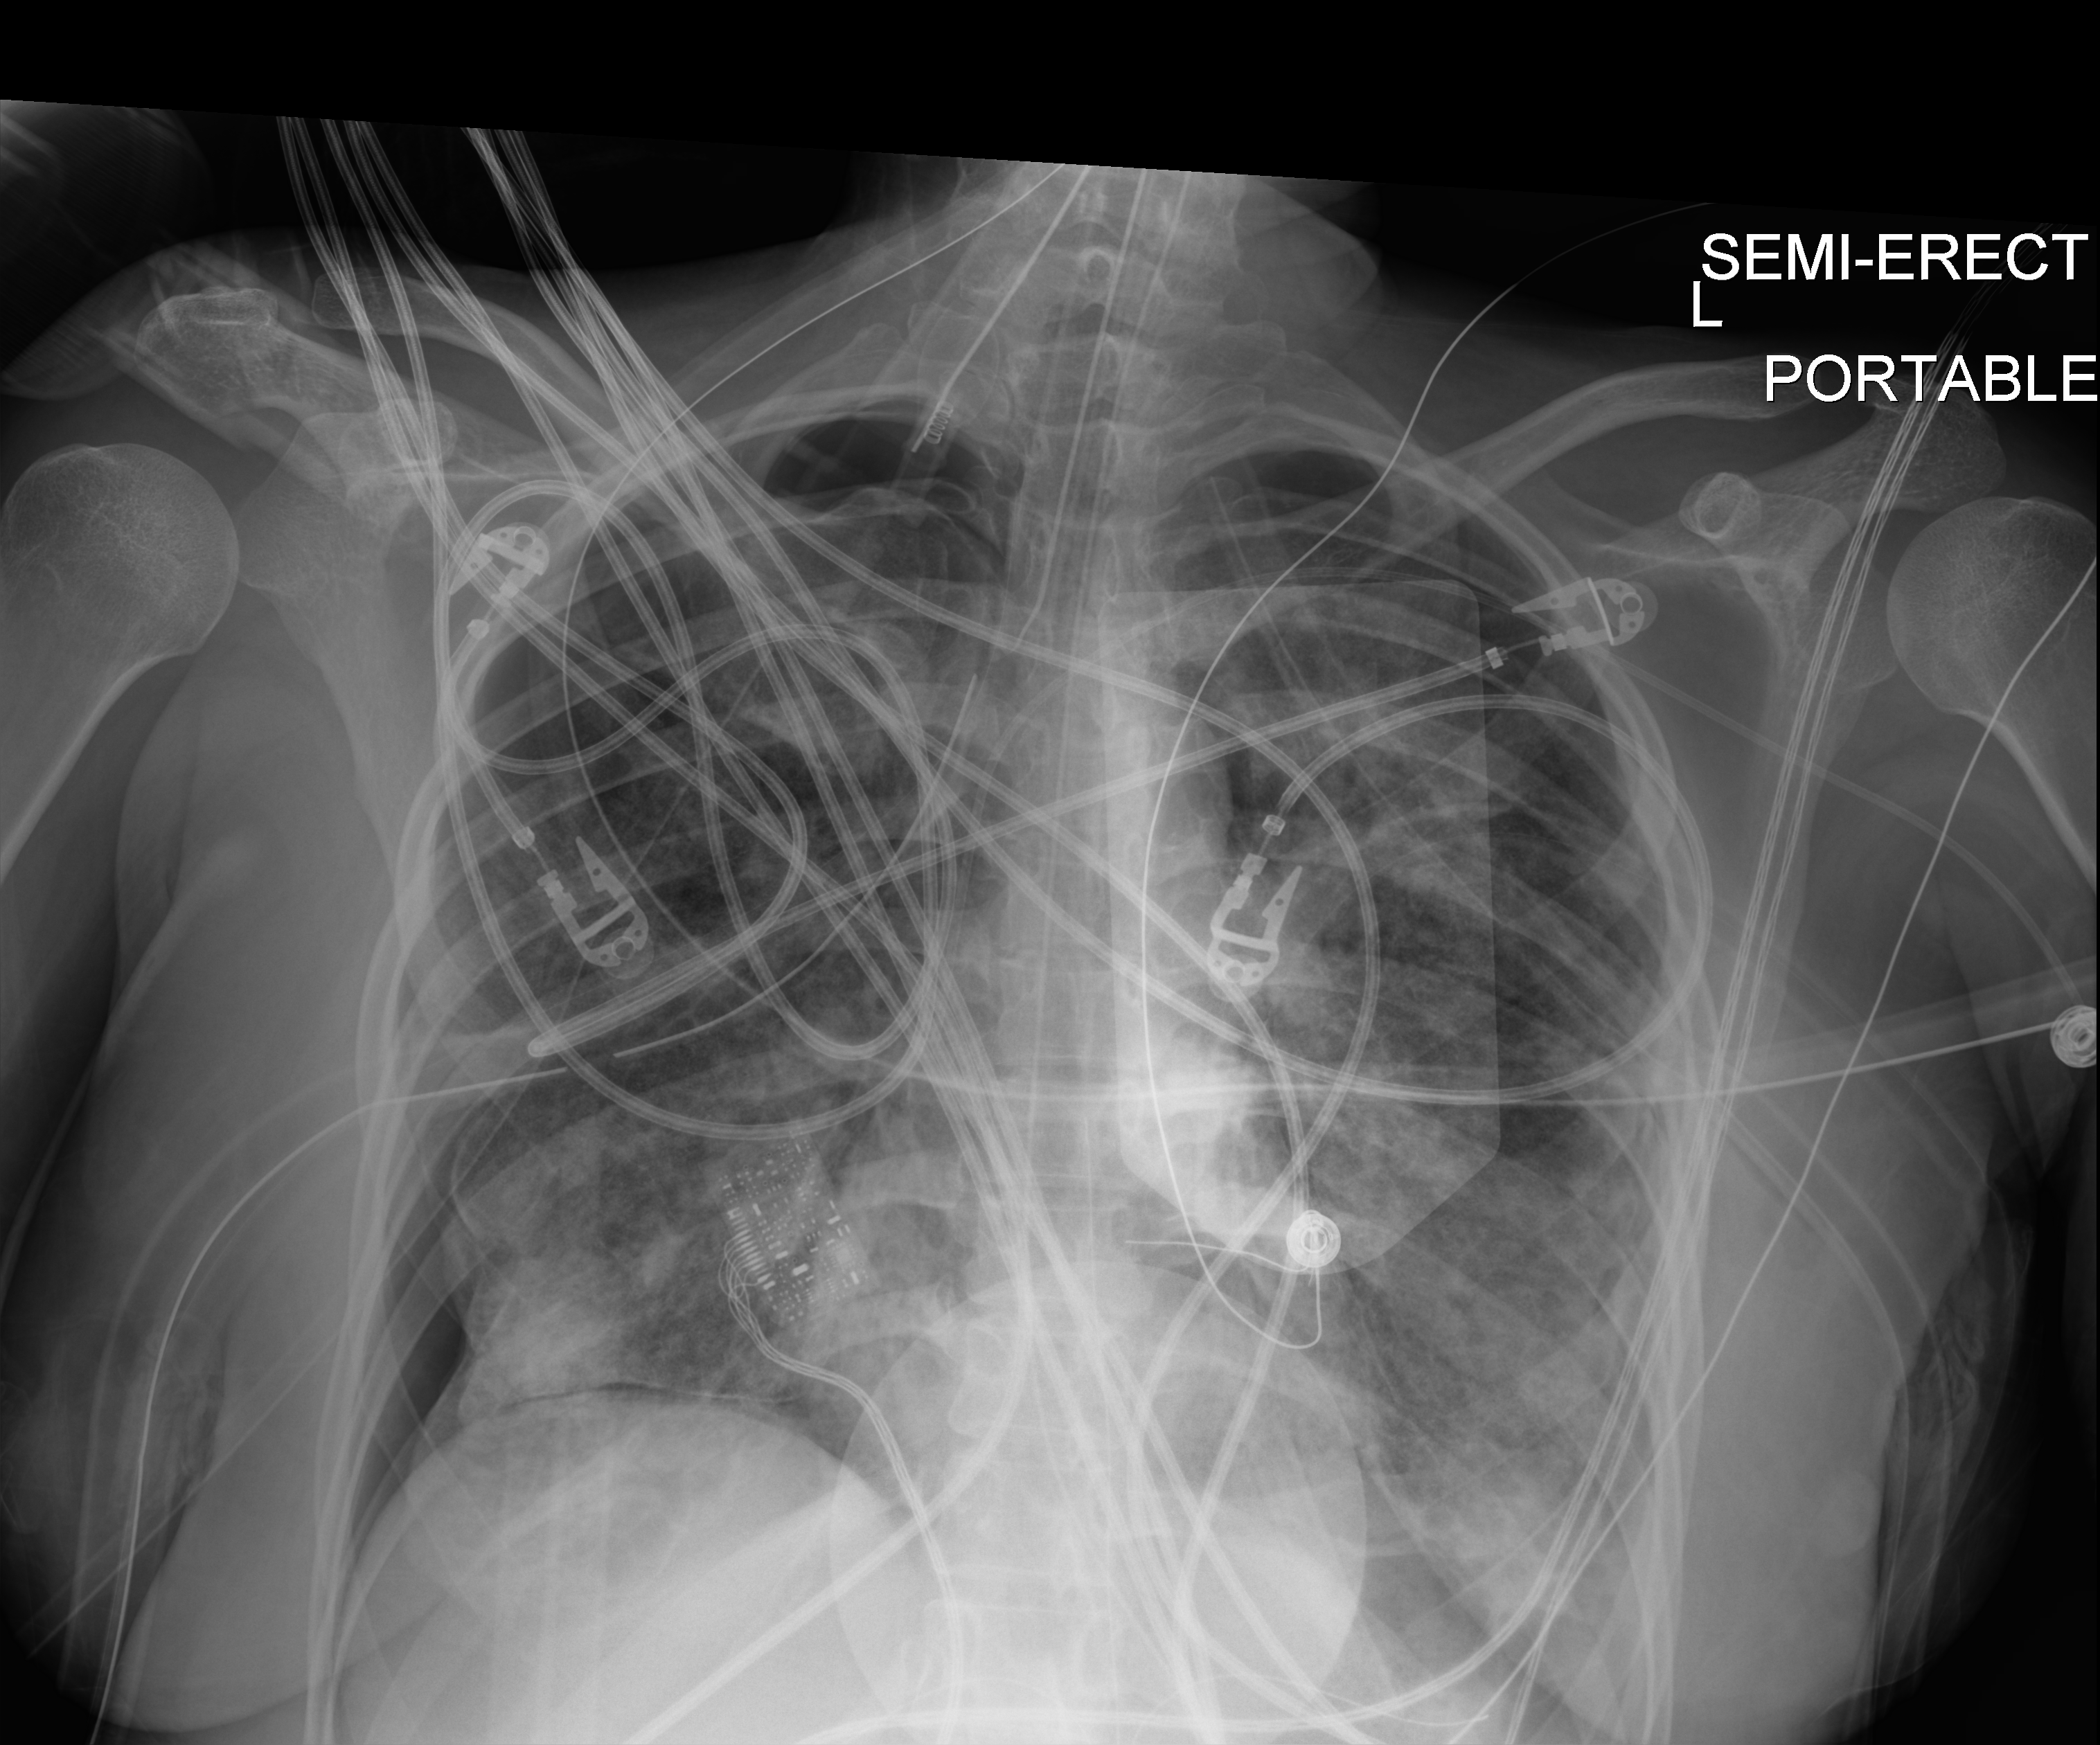
Bedside chest radiograph (digital radiography); anteroposterior (AP) projection. Patient hospitalised with COVID-19, aged 18–59 years.
From the hospital-stay record, not from the radiograph (when in the stay this image was taken is not recorded): other chronic lung disease (admission record): no; mechanically ventilated during this hospital stay: yes; hypertension (admission record): no.